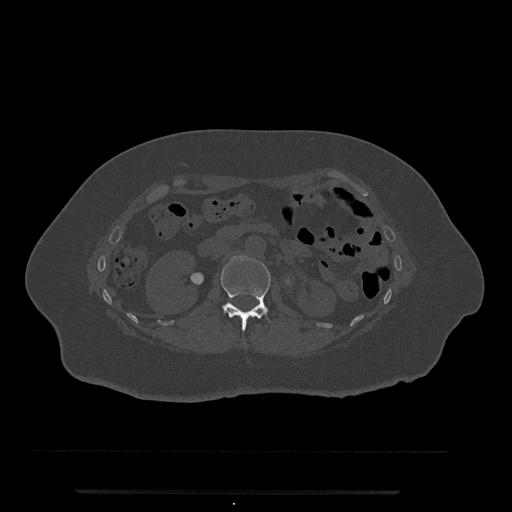
CT including the spine, one axial slice; 120 kVp; bone window (W 1800 / L 400 HU); 512 × 512 image matrix. Female patient, age 51 years. From the clinical record (not read from this slice): primary cancer: neuro; vertebrae with lytic lesions (as recorded): T8.
Structures marked on this image (semi-automatically segmented with operator editing):
- L1 vertebra: bounding box [x1, y1, x2, y2] px = [221, 256, 271, 331]